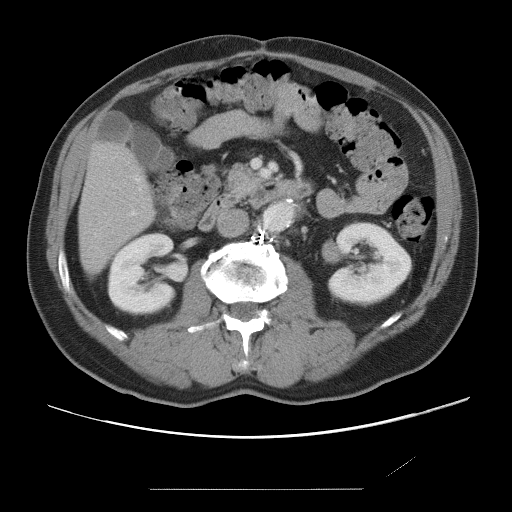
Contrast-enhanced abdominal CT, one axial slice; position 22 of 87 along the scan axis; soft-tissue window (W 400 / L 40 HU); 5 mm slice thickness; 512 × 512 image matrix, field of view 406 × 406 mm. Male patient, age 74 years. From the clinical record (not read from this slice): diagnosis: colorectal cancer liver metastases, imaged before liver resection; multiple liver metastases: yes; largest metastasis: 1.1 cm; disease in both lobes: no.
Structures marked on this image (outlined manually by an expert reader):
- hepatic veins: bounding box (x1, y1, x2, y2) in pixels: (136, 178, 141, 189)
- liver: (79, 144, 151, 273)
- planned liver remnant (the part of the liver to remain after resection): (79, 145, 152, 273)
- portal vein (with intrahepatic branches): (132, 211, 136, 215)